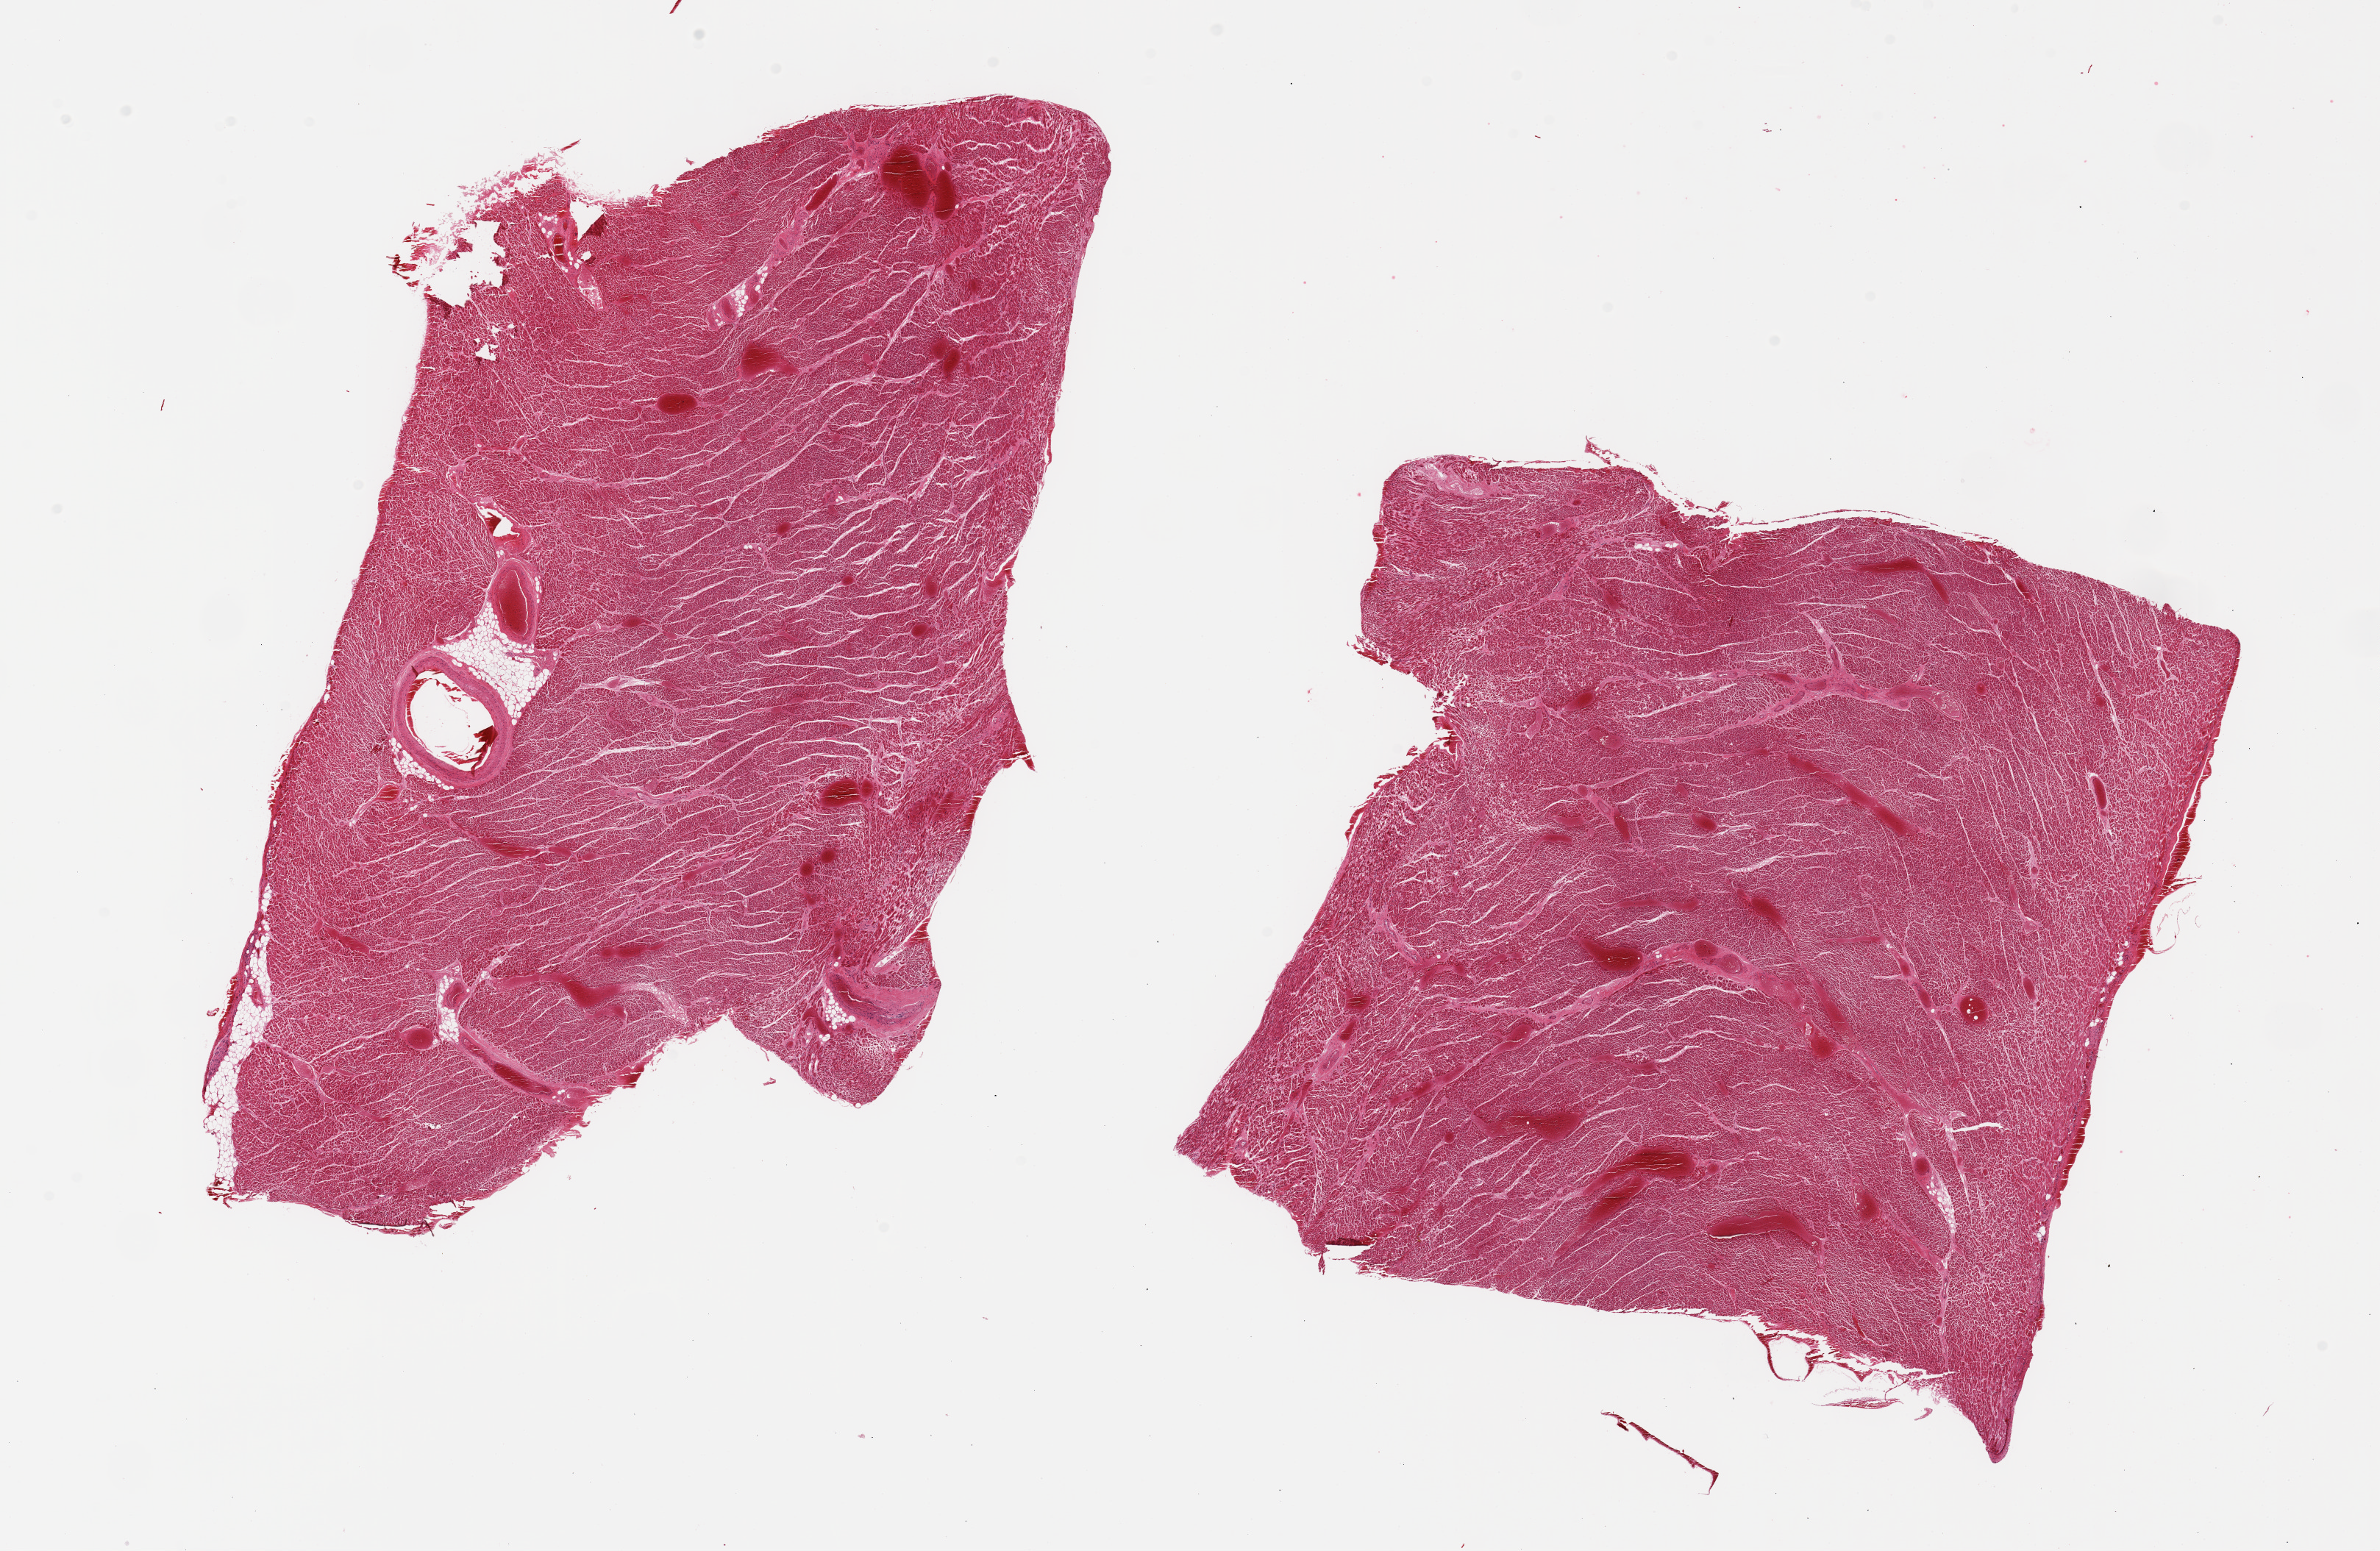
Digitized H&E-stained section, shown as a low-resolution overview of the whole scanned area (about 25.6 x 16.7 mm), PAXgene-fixed paraffin-embedded (PFPE) section, section of heart (target tissue), tissue donor sample. Donor: male.
* pathologist's review note for this sample: 2 pieces; severe congestion